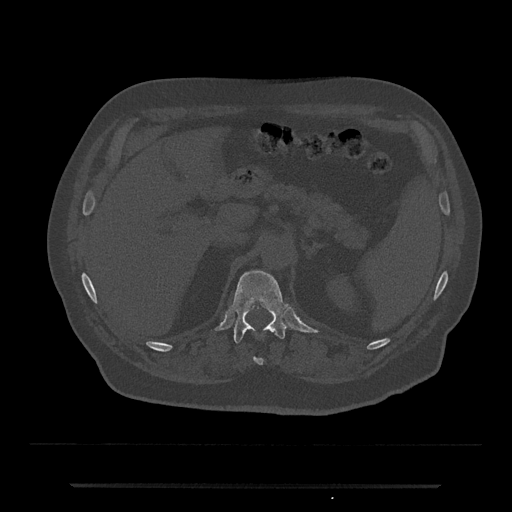
CT including the spine, one axial slice. Position 602 of 797 along the scan axis. 120 kVp. Bone window (W 1800 / L 400 HU). 0.5 mm slice thickness. 512 × 512 image matrix. Male patient, age 80 years. Case-level facts recorded for this patient, not image findings: primary cancer: prostate; vertebrae with lytic lesions (as recorded): L1, T11.
Outlined on this slice (semi-automatically segmented with operator editing):
- T11 vertebra: bounding box (x1, y1, x2, y2) in pixels: (254, 358, 264, 365)
- T12 vertebra: (231, 270, 288, 343)